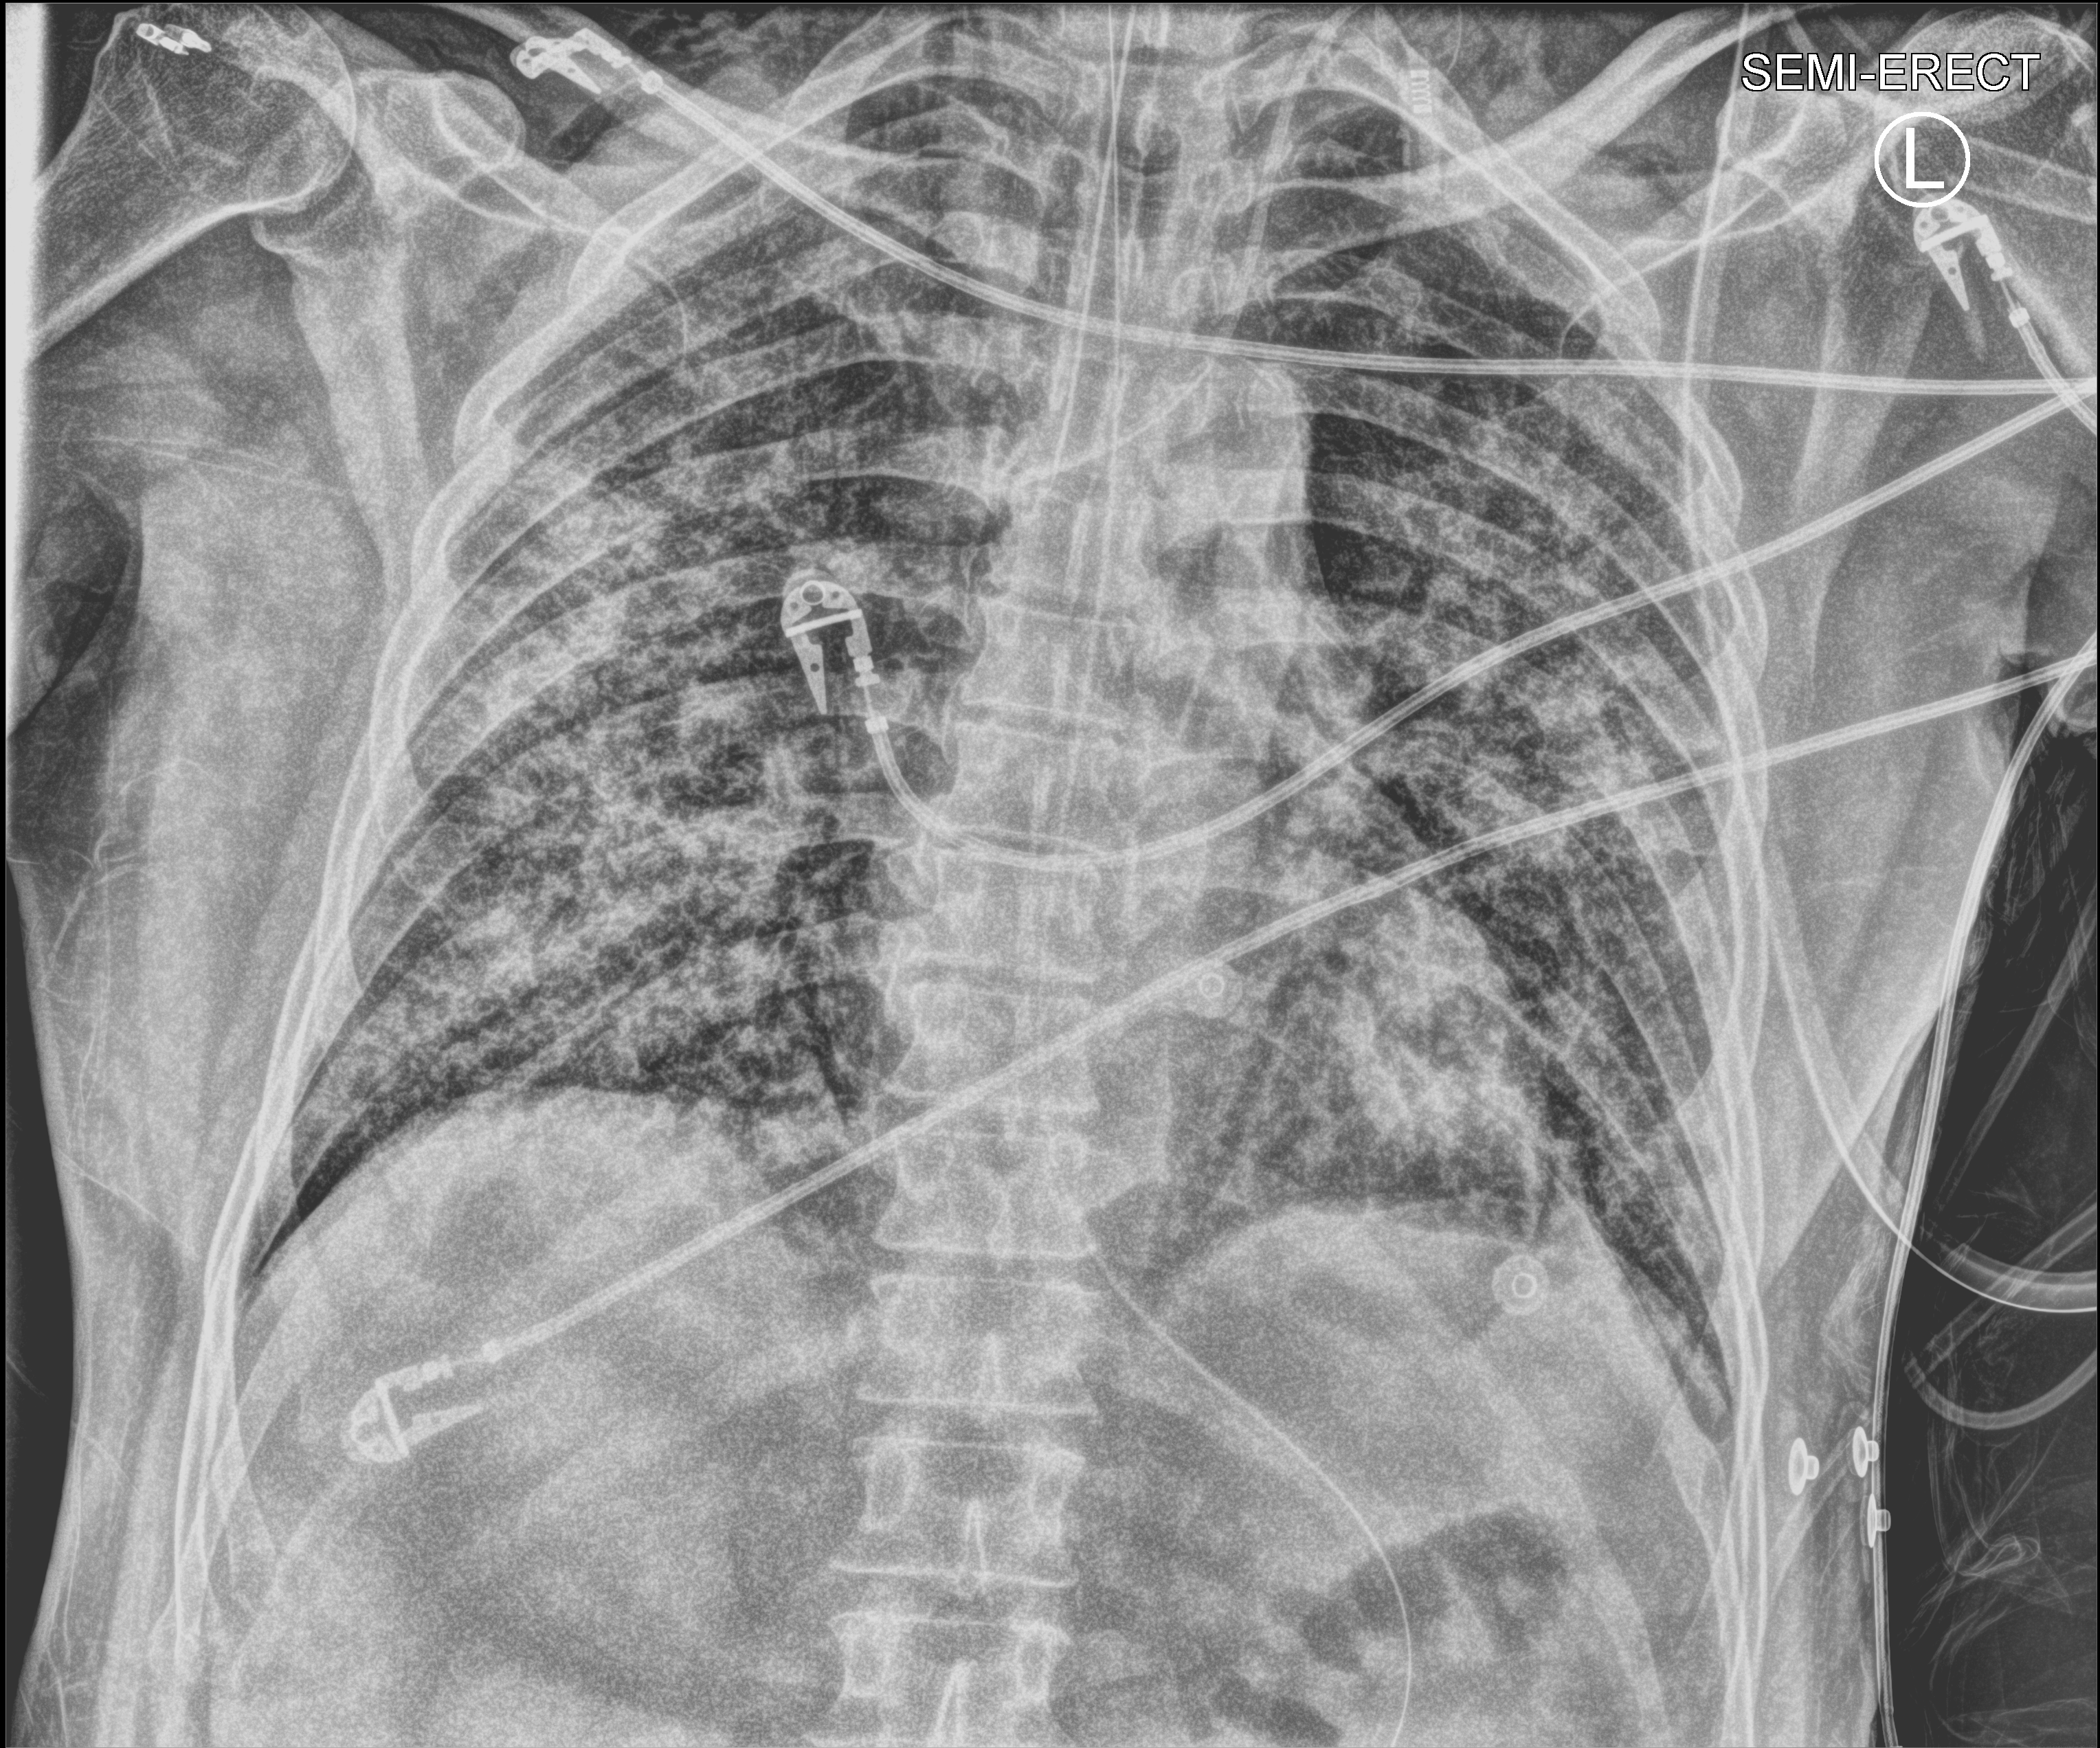
Bedside chest radiograph (computed radiography). Patient hospitalised with COVID-19; male, aged 60–74 years.
Hospital-stay facts (about this admission, not read from this image; timing relative to this image not recorded):
- mechanically ventilated during this hospital stay: yes